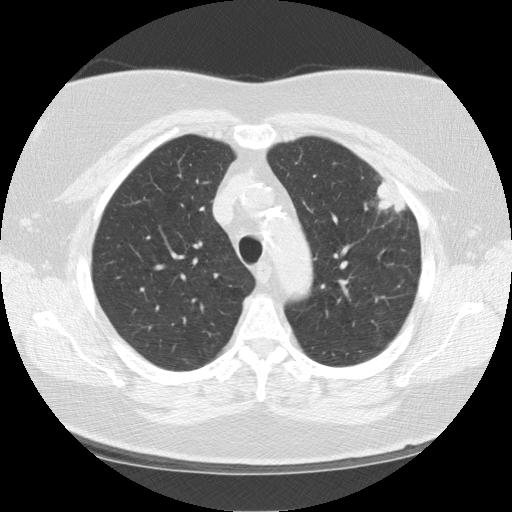
Low-dose screening chest CT, axial slice; baseline screening round; lung window (W 1500 / L -600 HU); 2.5 mm slice thickness; standard (soft-tissue) reconstruction kernel (STANDARD); 120 kVp; 512 × 512 image matrix. Female, age 67 years at enrolment. Former smoker at enrolment.
Expert reader's lesion annotation, bounding box [x1, y1, x2, y2] px = [350, 164, 420, 228]. Reader record for this screening exam (exam-level; its link to the box is not recorded): non-calcified nodule or mass ≥4 mm, left upper lobe, 28 × 19 mm, soft tissue attenuation. Official screen result: positive, change unspecified: nodule(s) >= 4 mm or enlarging nodule(s), mass(es), or other non-specific abnormalities suspicious for lung cancer. Later outcome: lung cancer diagnosed 33 days after this screen — squamous cell carcinoma, NOS, left upper lobe, poorly differentiated (G3), stage IA (AJCC 6th edition), 25 mm at pathology.